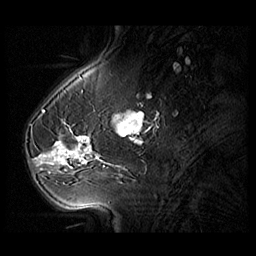
Breast MRI (dynamic contrast-enhanced), one sagittal slice. Position 32 of 104 along the scan axis. 3 images stored at this slice position (order not interpretable as contrast timing). 1.5 T. TE 1.3 ms, TR 5.5 ms. 256 × 256 image matrix, field of view 220 × 220 mm. Patient: female, 54 years. From the clinical record (not read from this slice): setting: breast cancer imaged before/during neoadjuvant chemotherapy; receptor status: HR-positive, HER2-negative.
Annotated regions visible in this slice (semi-automatically segmented with operator editing):
- analysis volume of interest (the breast-tissue region the enhancement analysis was run in; not a lesion): bounding box (x1, y1, x2, y2) in pixels: (28, 127, 104, 182)
- tumour enhancement mask (voxels above the 140 % enhancement threshold inside the analysis volume of interest): (36, 135, 97, 165)